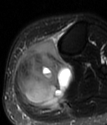
MRI of an extremity soft-tissue mass, one axial slice; position 32 of 78 along the scan axis; T2-weighted fat-saturated; MR volume resampled by the dataset authors to the PET/CT grid (not the native acquisition matrix); 3.27 mm slice thickness; 107 × 125 image matrix, field of view 104 × 122 mm. Female patient. From the clinical record (not read from this slice): histological type: extraskeletal high grade osteogenic sarcoma; grade: high; site of the primary tumour: left calf.
Outlined on this slice (expert contour drawn on MRI and transferred to this co-registered scan by the dataset authors):
- gross tumour volume (mass): bounding box (x1, y1, x2, y2) in pixels: (17, 40, 72, 108)